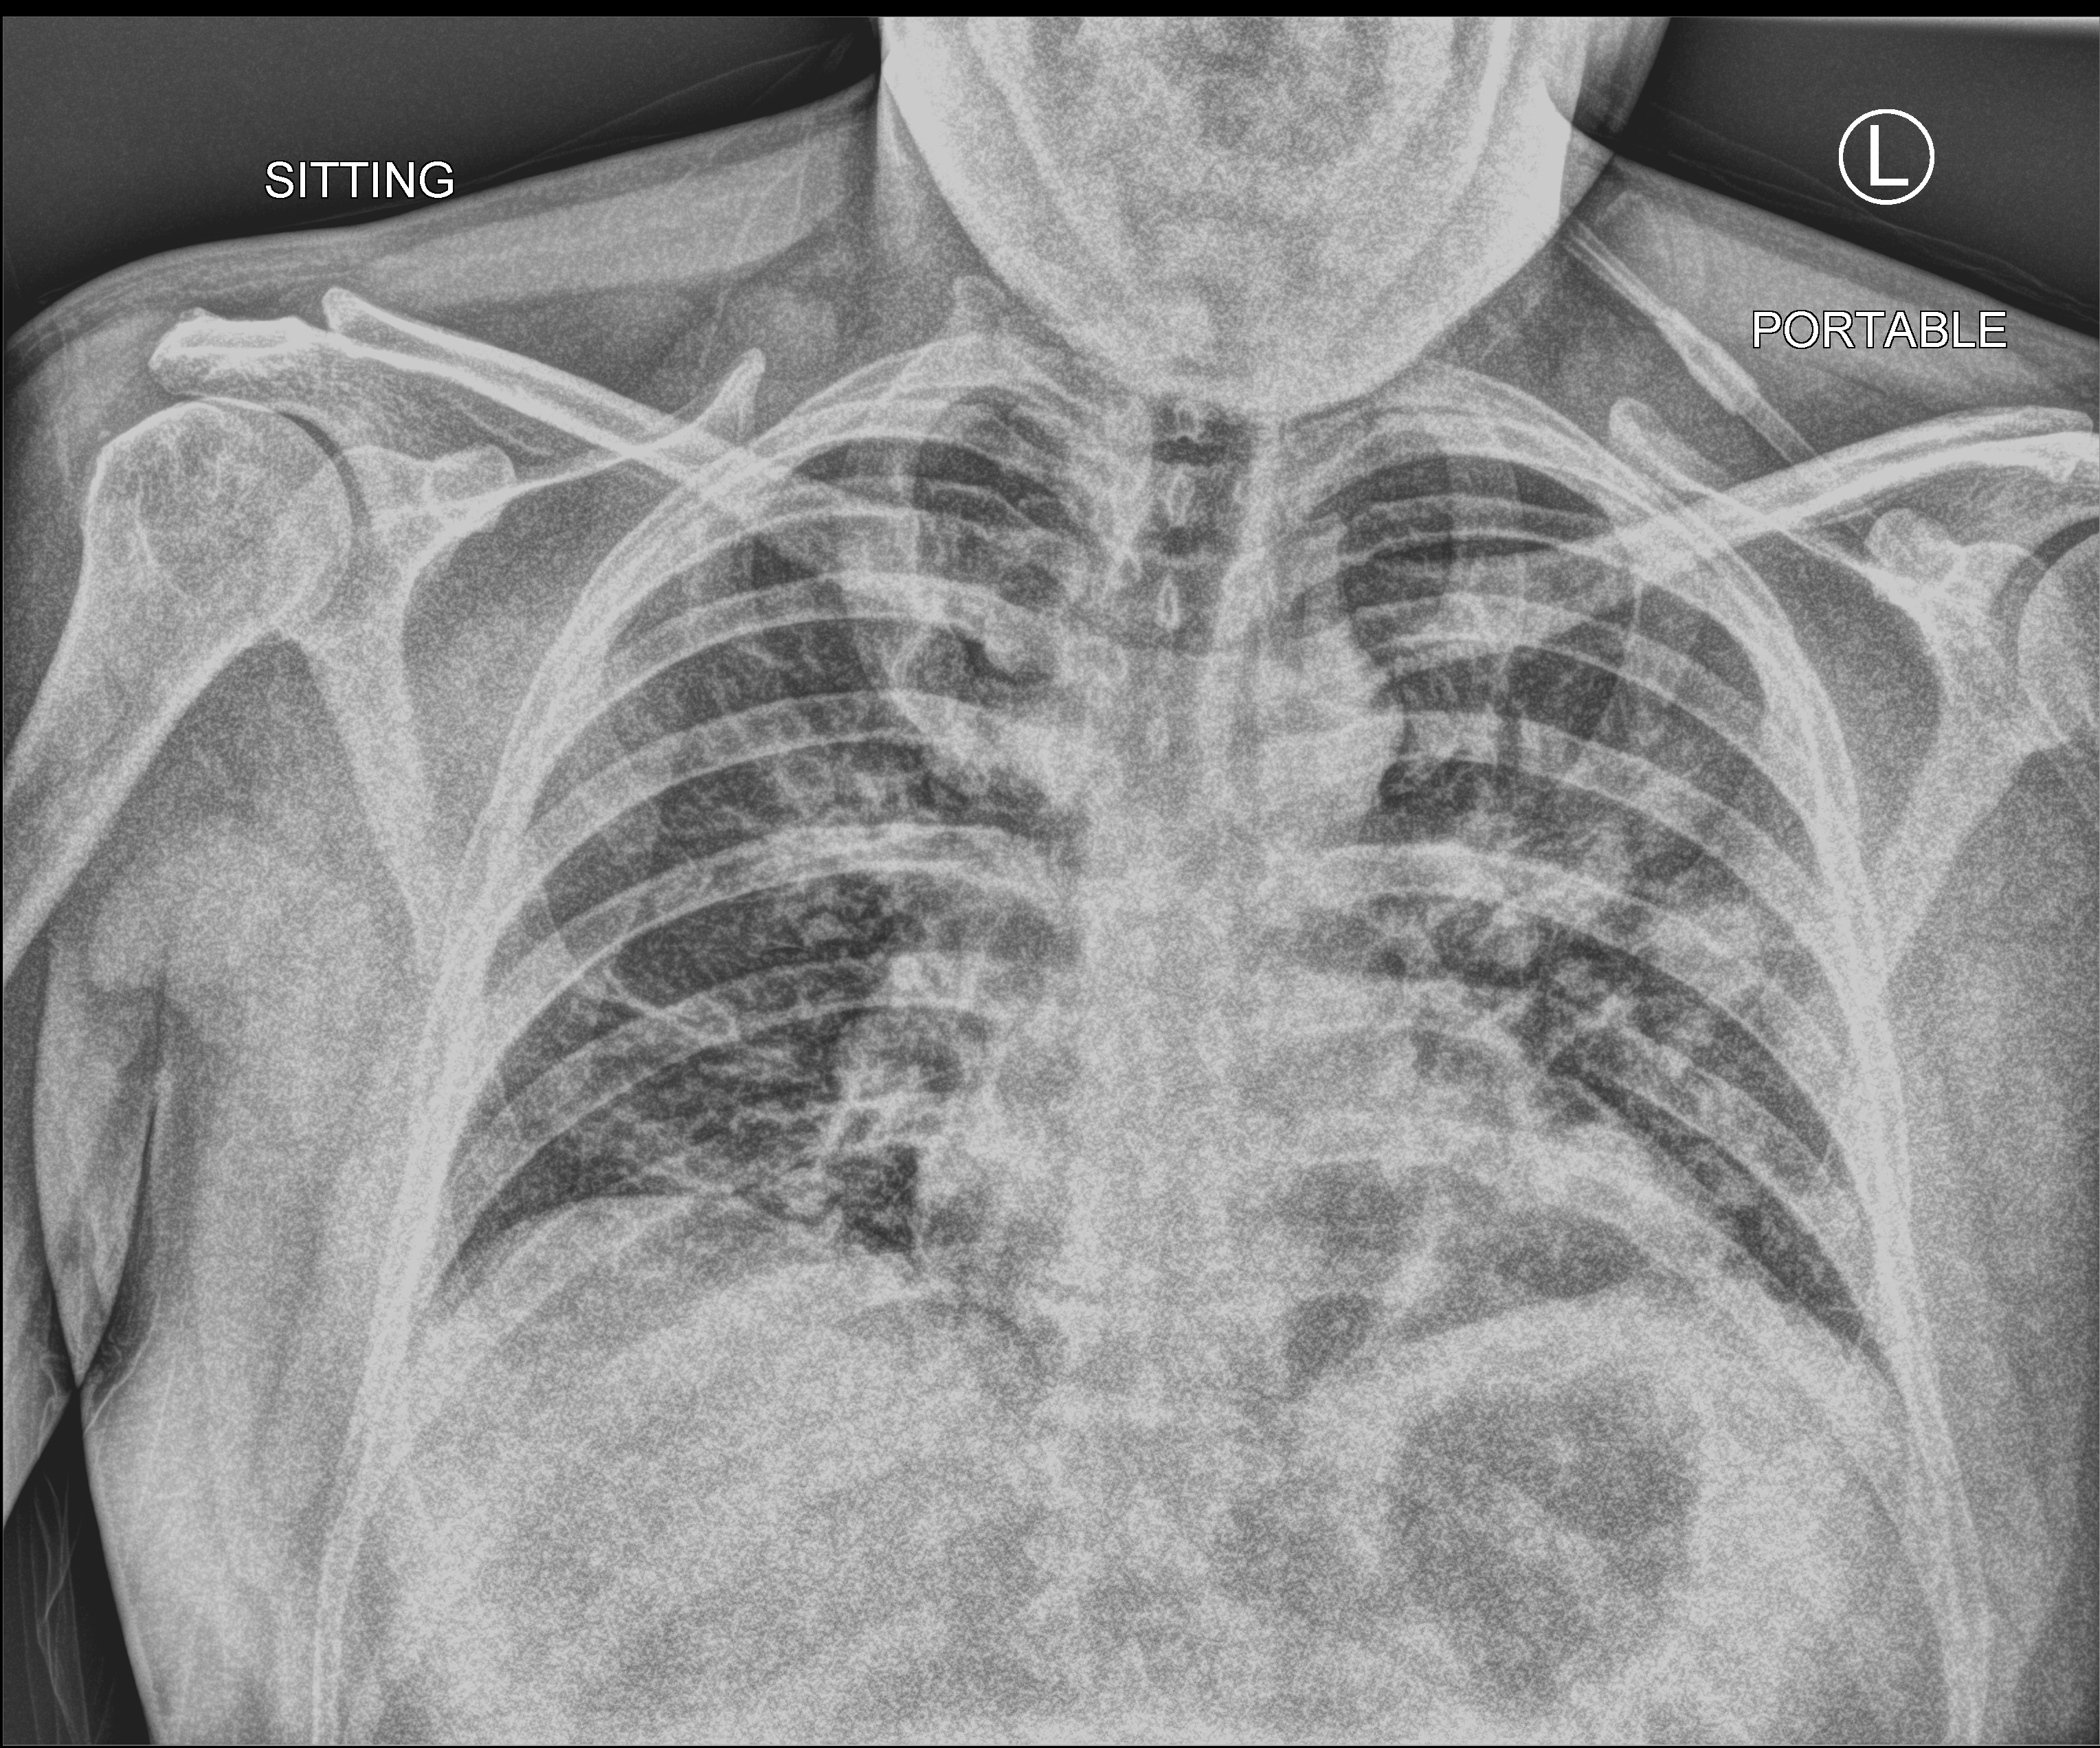
Portable chest radiograph. Male patient hospitalised with COVID-19, age 18–59 years.
From the hospital-stay record, not from the radiograph (when in the stay this image was taken is not recorded):
- mechanically ventilated during this hospital stay: yes